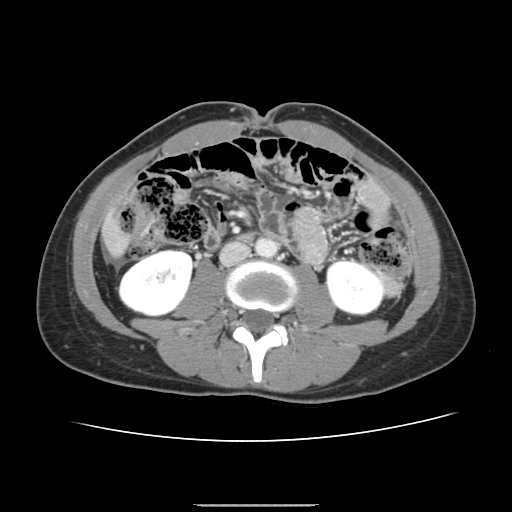
Contrast-enhanced abdominal CT, one axial slice. Slice 35 of 150 in the series (ordered by position). 120 kVp. Intravenous contrast given. Soft-tissue window (W 400 / L 40 HU). 512 × 512 image matrix, field of view 324 × 324 mm. Female patient, age 32 years. From the clinical record (not read from this slice): diagnosis: colorectal cancer liver metastases, imaged before liver resection; multiple liver metastases: yes; largest metastasis: 0.7 cm; disease in both lobes: no.
Annotated regions visible in this slice (expert manual segmentation):
- liver: bounding box <107,227,125,253> (left, top, right, bottom; pixels)
- planned liver remnant (the part of the liver to remain after resection): <107,225,125,253>